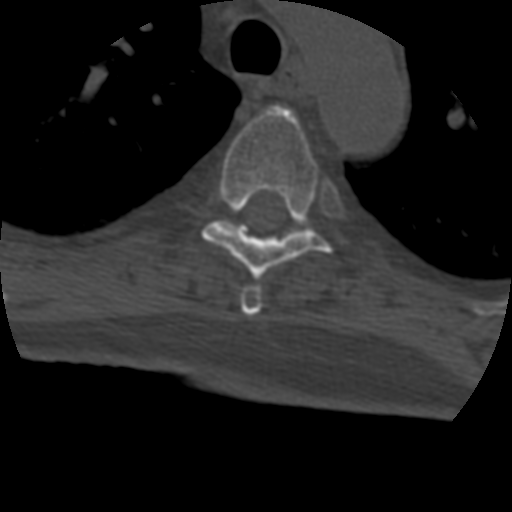
CT including the spine, one axial slice. Slice 319 of 399 in the series (ordered by position). Reconstruction kernel STANDARD. Bone window (W 1800 / L 400 HU). 512 × 512 image matrix, field of view 160 × 160 mm. Patient age 69 years. Case-level facts recorded for this patient, not image findings: primary cancer: prostate.
Outlined on this slice (semi-automatic segmentation, software-assisted and operator-edited):
- T4 vertebra: bounding box <241,287,262,316> (left, top, right, bottom; pixels)
- T5 vertebra: <201,106,348,281>